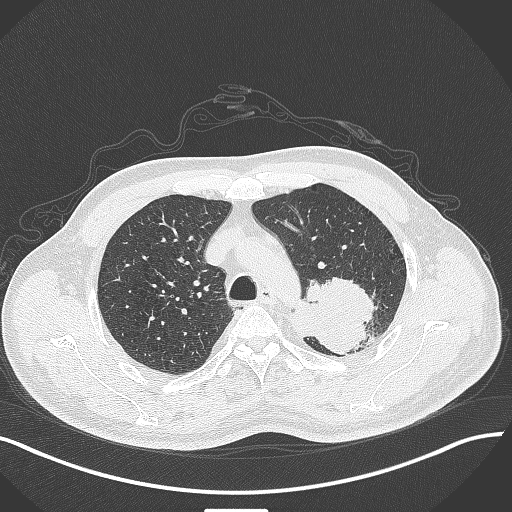
Chest CT, one axial slice. Slice 324 of 429 in the series (ordered by position). 120 kVp. Lung window (W 1500 / L -600 HU). 1 mm slice thickness. 512 × 512 image matrix, field of view 400 × 400 mm. Patient: male, 55 years. Case-level facts recorded for this patient, not image findings: clinical TNM (as recorded): T3 N0 M1c.
Annotated regions visible in this slice (bounding box drawn by a radiologist):
- lung tumour (recorded histology: adenocarcinoma): box from (x=288, y=272) to (x=378, y=357) px